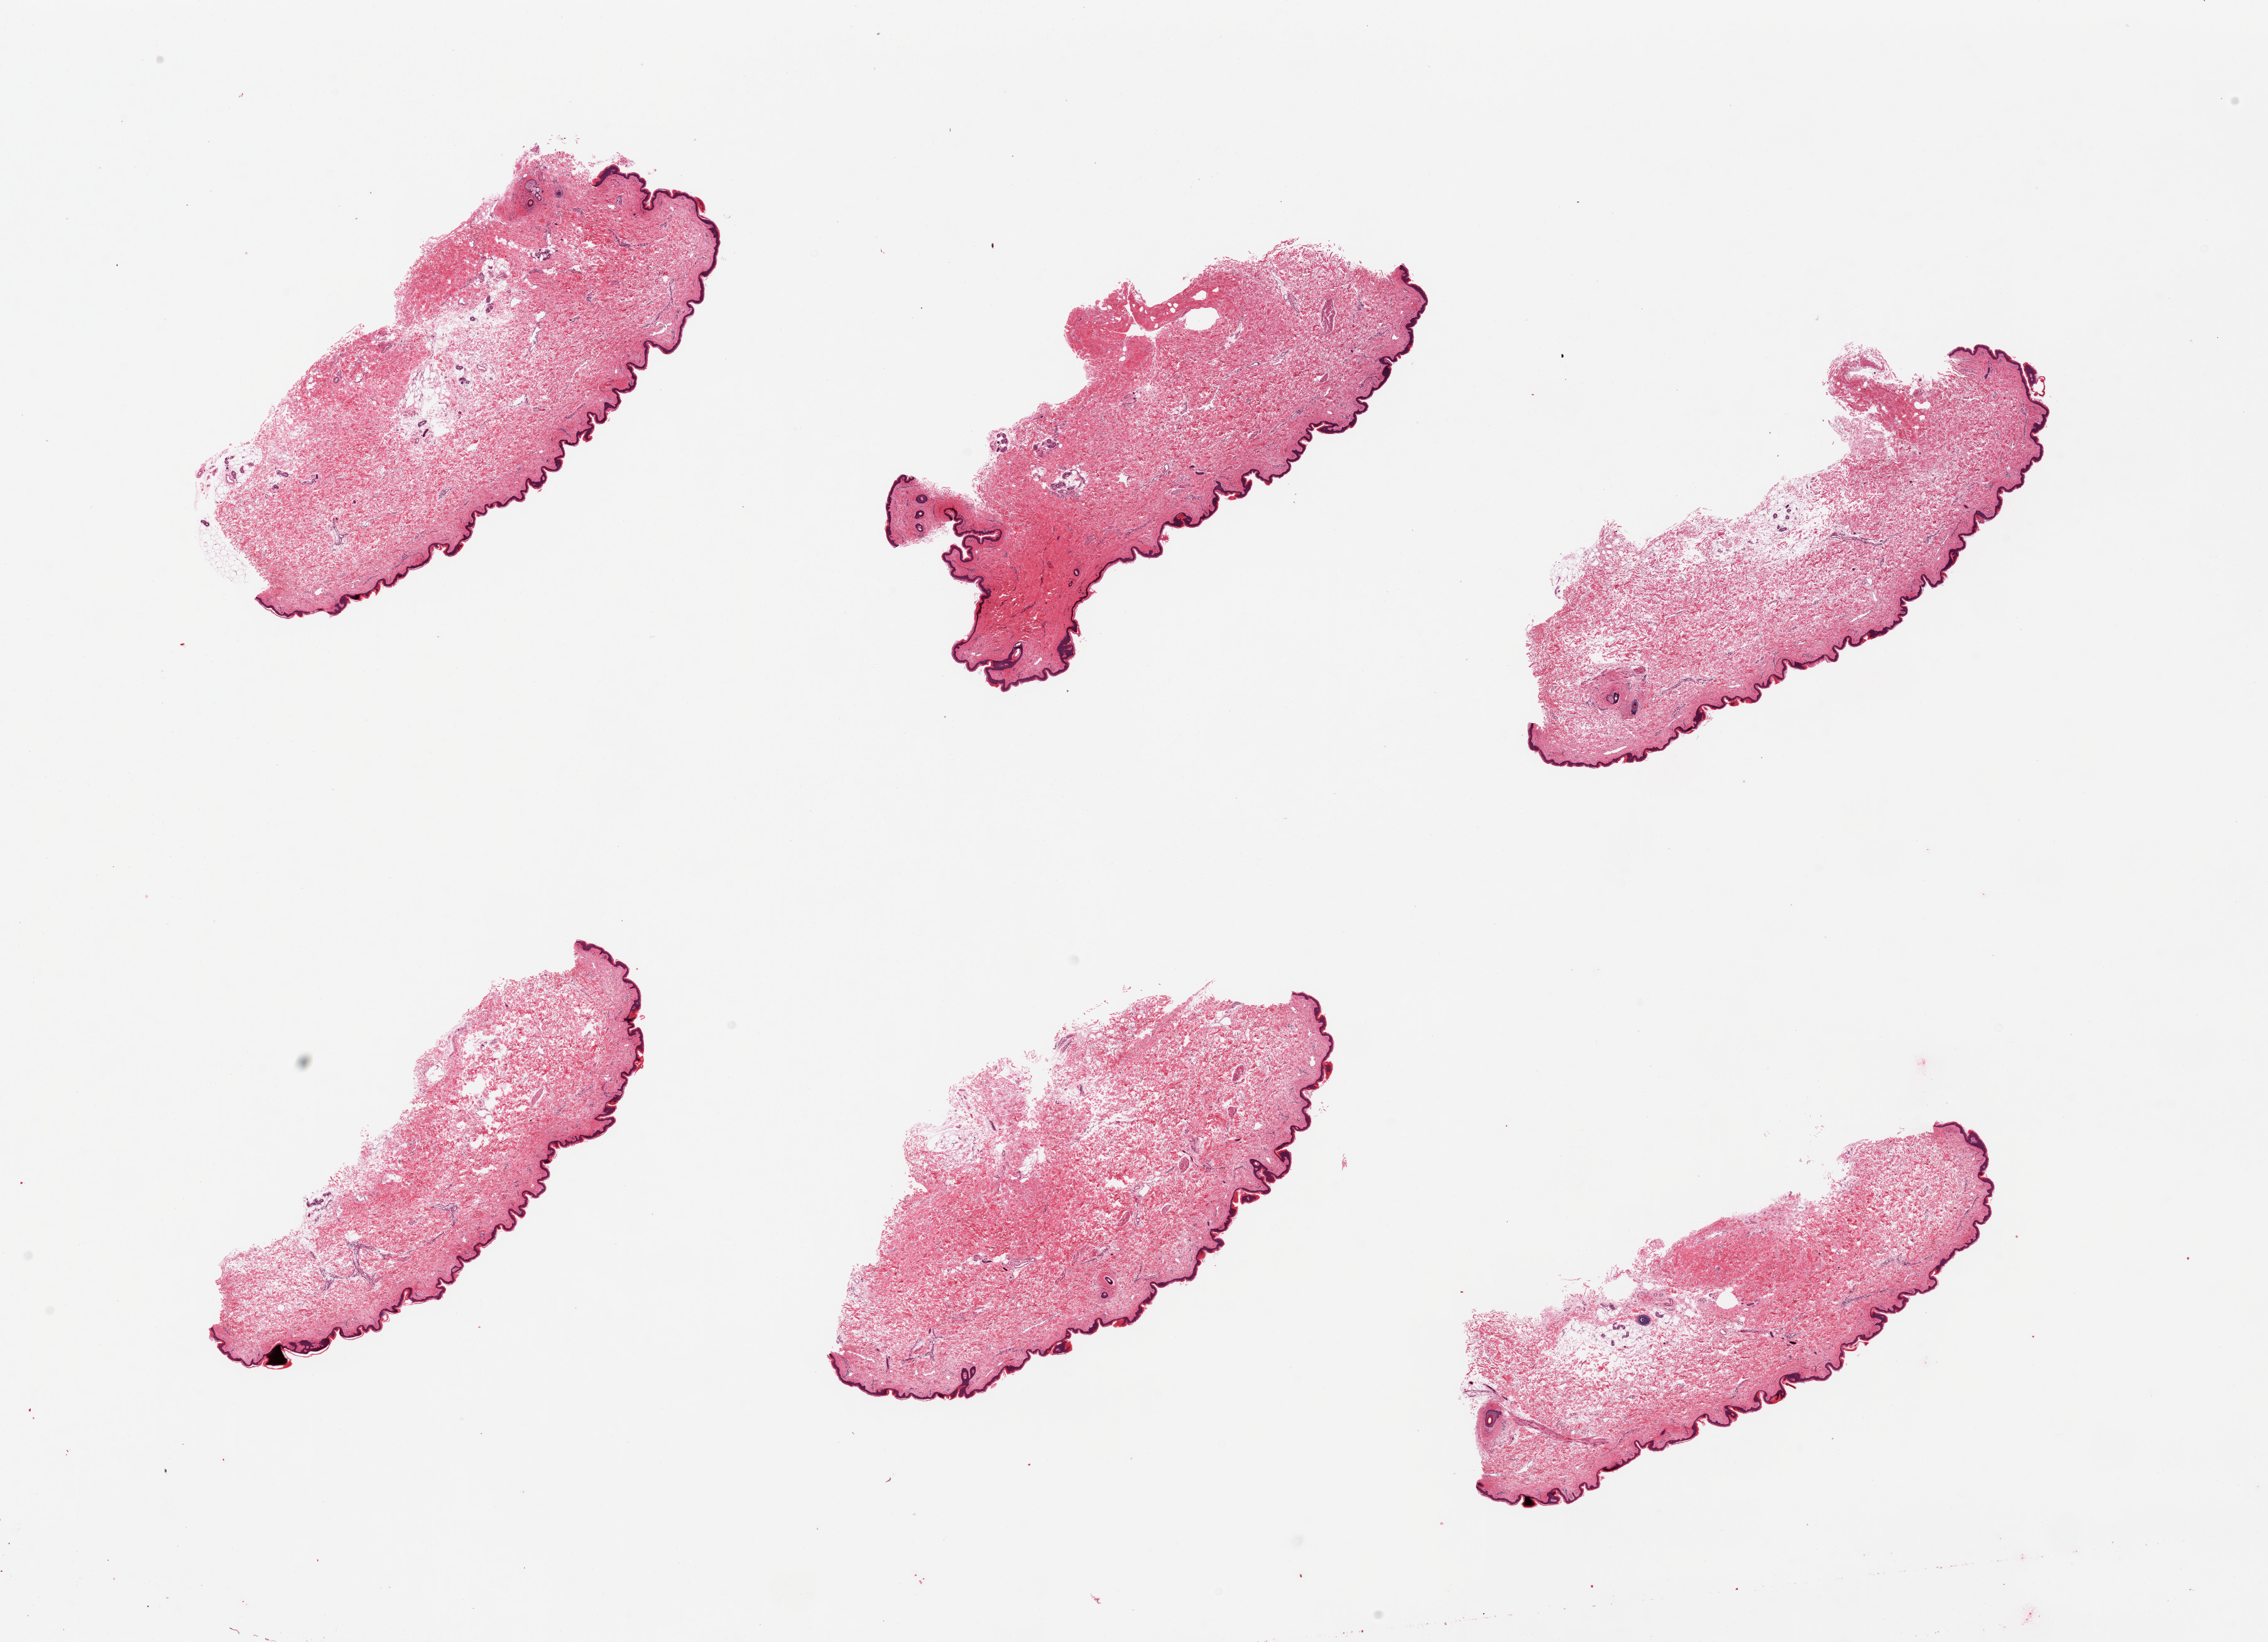
Digitized haematoxylin and eosin-stained section, brightfield — low-resolution overview of the scanned area, about 28.5 x 20.7 mm (from a 20x scan). PAXgene-fixed, paraffin-embedded tissue. Sampled site (target tissue): skin of suprapubic region. Tissue donor sample. Donor sex: female.
Pathologist's review note for this sample: 6 pieces; well trimmed.